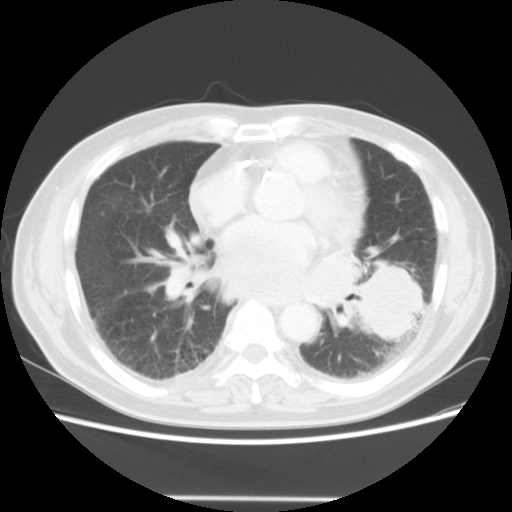
Chest CT, one axial slice; position 22 of 56 along the scan axis; reconstruction kernel STANDARD; 140 kVp; lung window (W 1500 / L -600 HU); 5 mm slice thickness; 512 × 512 image matrix. Patient: male, 66 years. Case-level facts recorded for this patient, not image findings: clinical TNM (as recorded): T4 N3 M0; histopathological grade: G3.
Outlined on this slice (rectangle marked by the reading radiologist):
- lung tumour (recorded histology: small cell carcinoma): box from (x=351, y=259) to (x=432, y=356) px